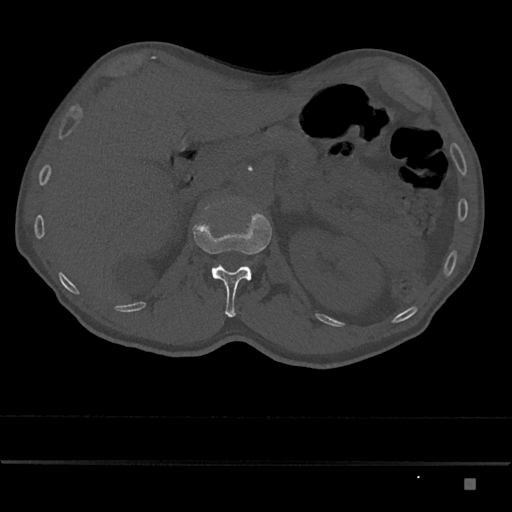
CT including the spine, one axial slice; reconstruction kernel Br40s/3; 120 kVp; bone window (W 1800 / L 400 HU); 0.5 mm slice thickness; 512 × 512 image matrix, field of view 390 × 390 mm. Patient: male, 72 years. Case-level facts recorded for this patient, not image findings: primary cancer: prostate.
Structures marked on this image (semi-automatically segmented with operator editing):
- L1 vertebra: bounding box <192,213,272,317> (left, top, right, bottom; pixels)